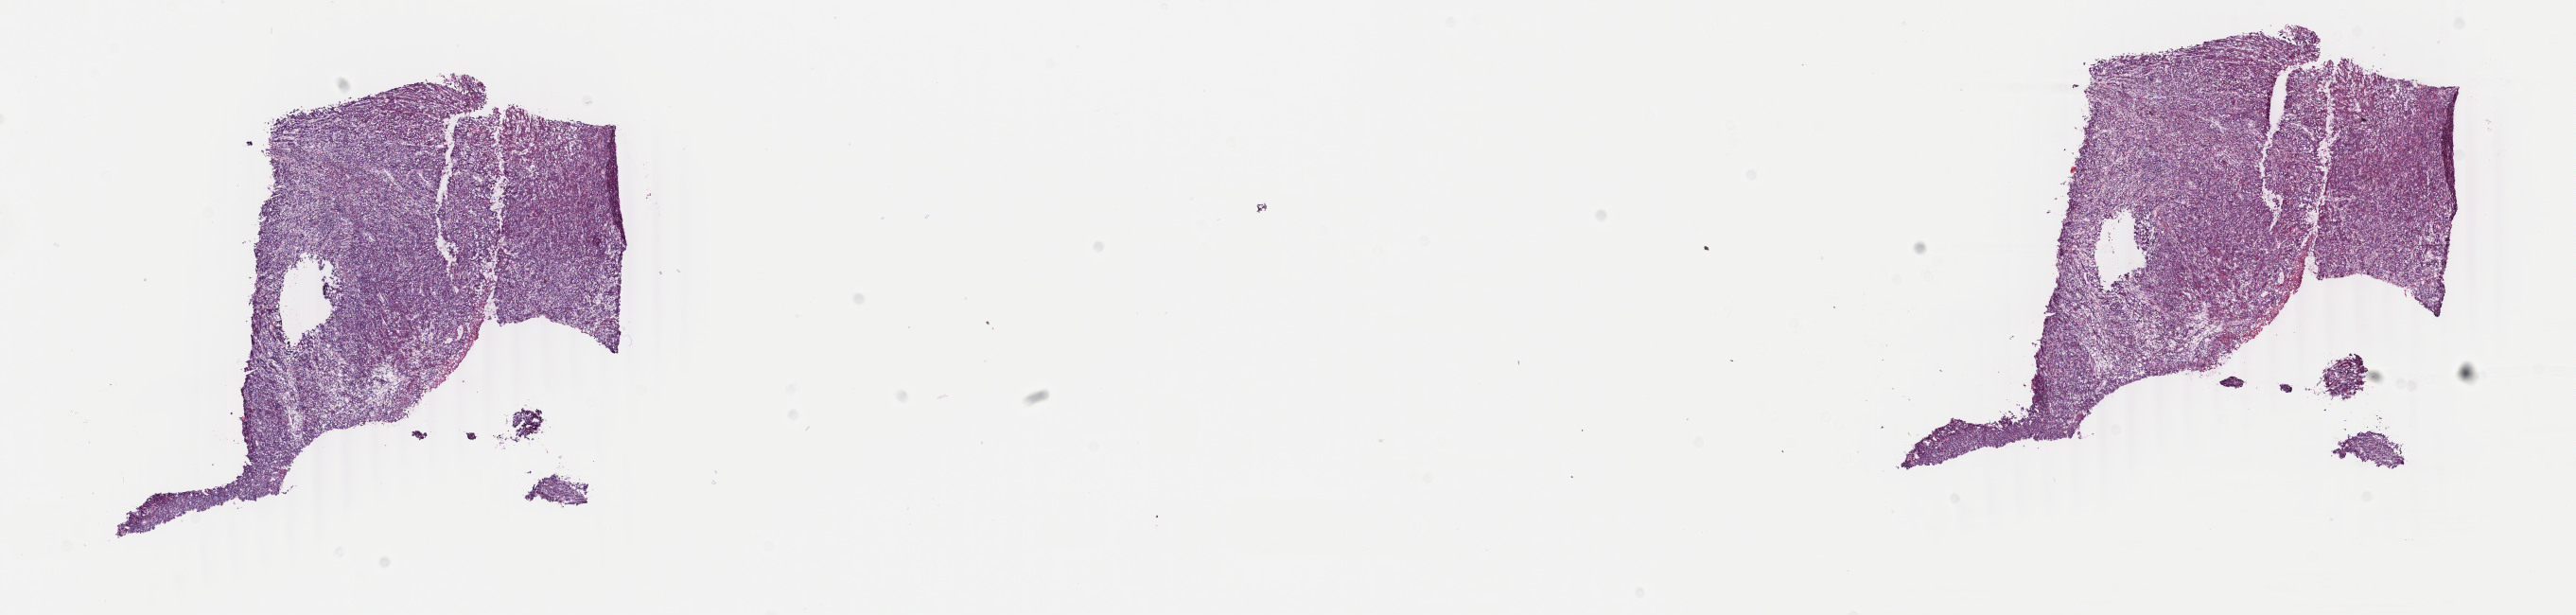
Whole-slide histology image, H&E, a low-resolution overview of the entire scanned area, about 21.7 x 5.2 mm (from a 40x scan); frozen section from the top of the tissue portion; primary tumour sample from the head and neck. Male, age 59 years at initial diagnosis. Histologic grade: G2 (moderately differentiated). Composition of this section per pathologist review: tumour cells 80%, tumour nuclei 80%, normal cells 0%, stromal cells 10%, necrosis 10%. Inflammatory infiltration, as recorded: lymphocyte infiltration 40%, monocyte infiltration 20%, neutrophil infiltration 20%.
Histologic diagnosis: Squamous cell carcinoma, NOS (tongue, NOS). TNM: T4a N2b M0. AJCC pathologic stage: IVA (7th edition).